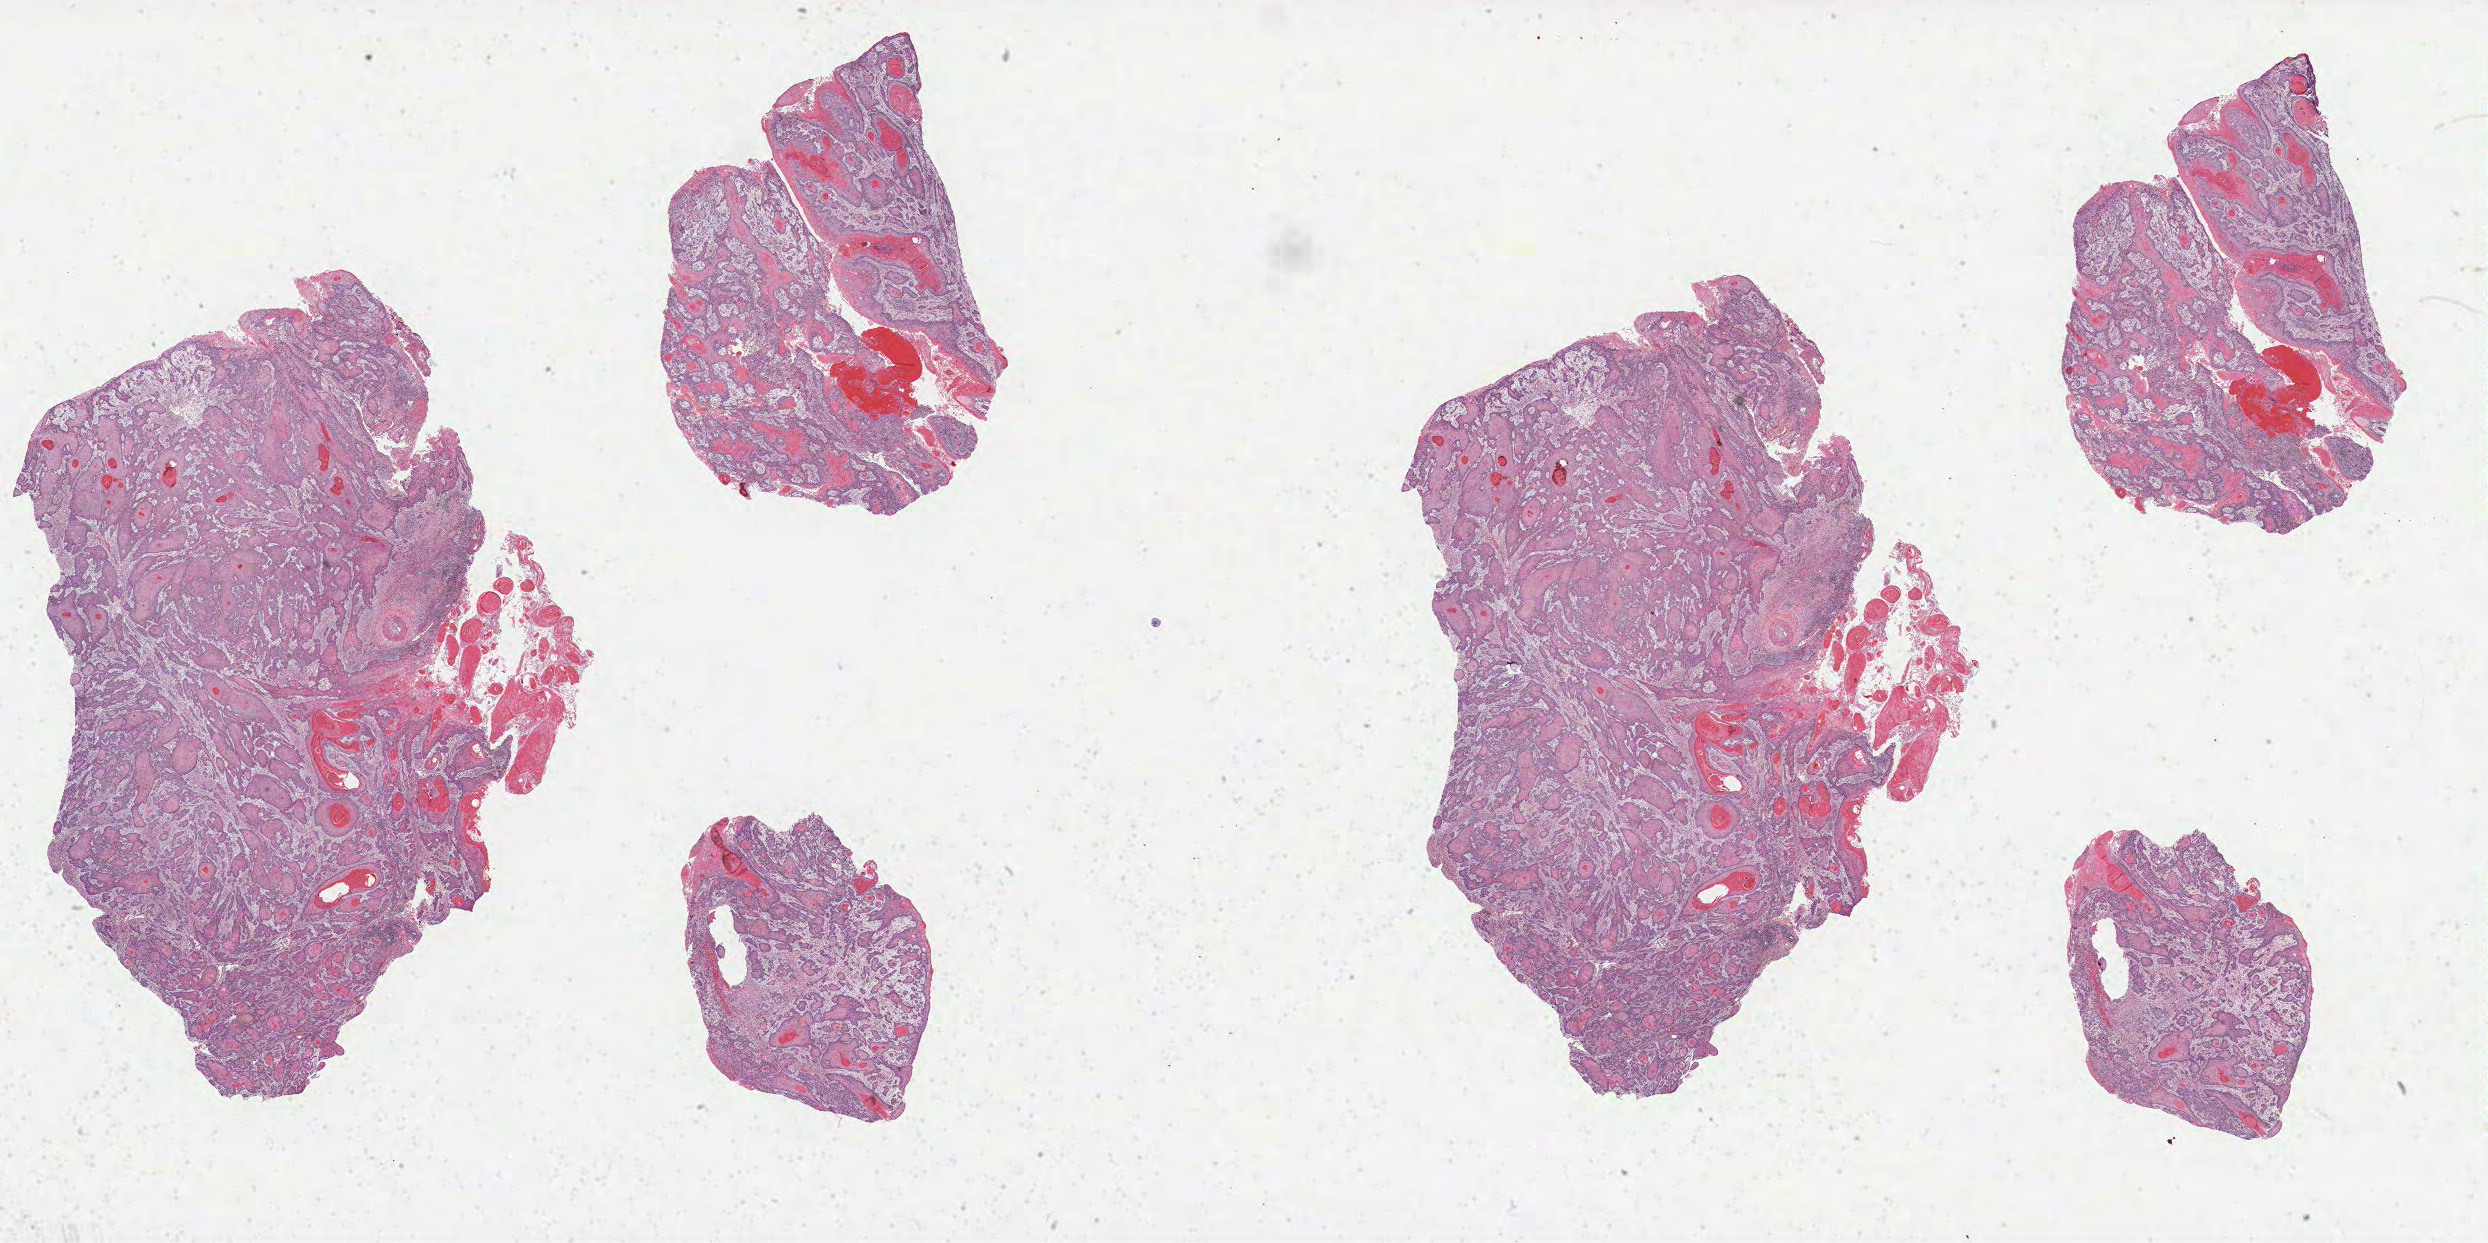
Whole-slide histology image, H&E, a low-resolution overview of the entire scanned area, about 40.1 x 20.0 mm, FFPE section, head and neck, primary tumour sample. Female, age 48 years at initial diagnosis. Histologic grade: G3 (poorly differentiated).
Diagnosis: Squamous cell carcinoma, NOS (tongue, NOS). AJCC pathologic stage: IVA (6th edition).